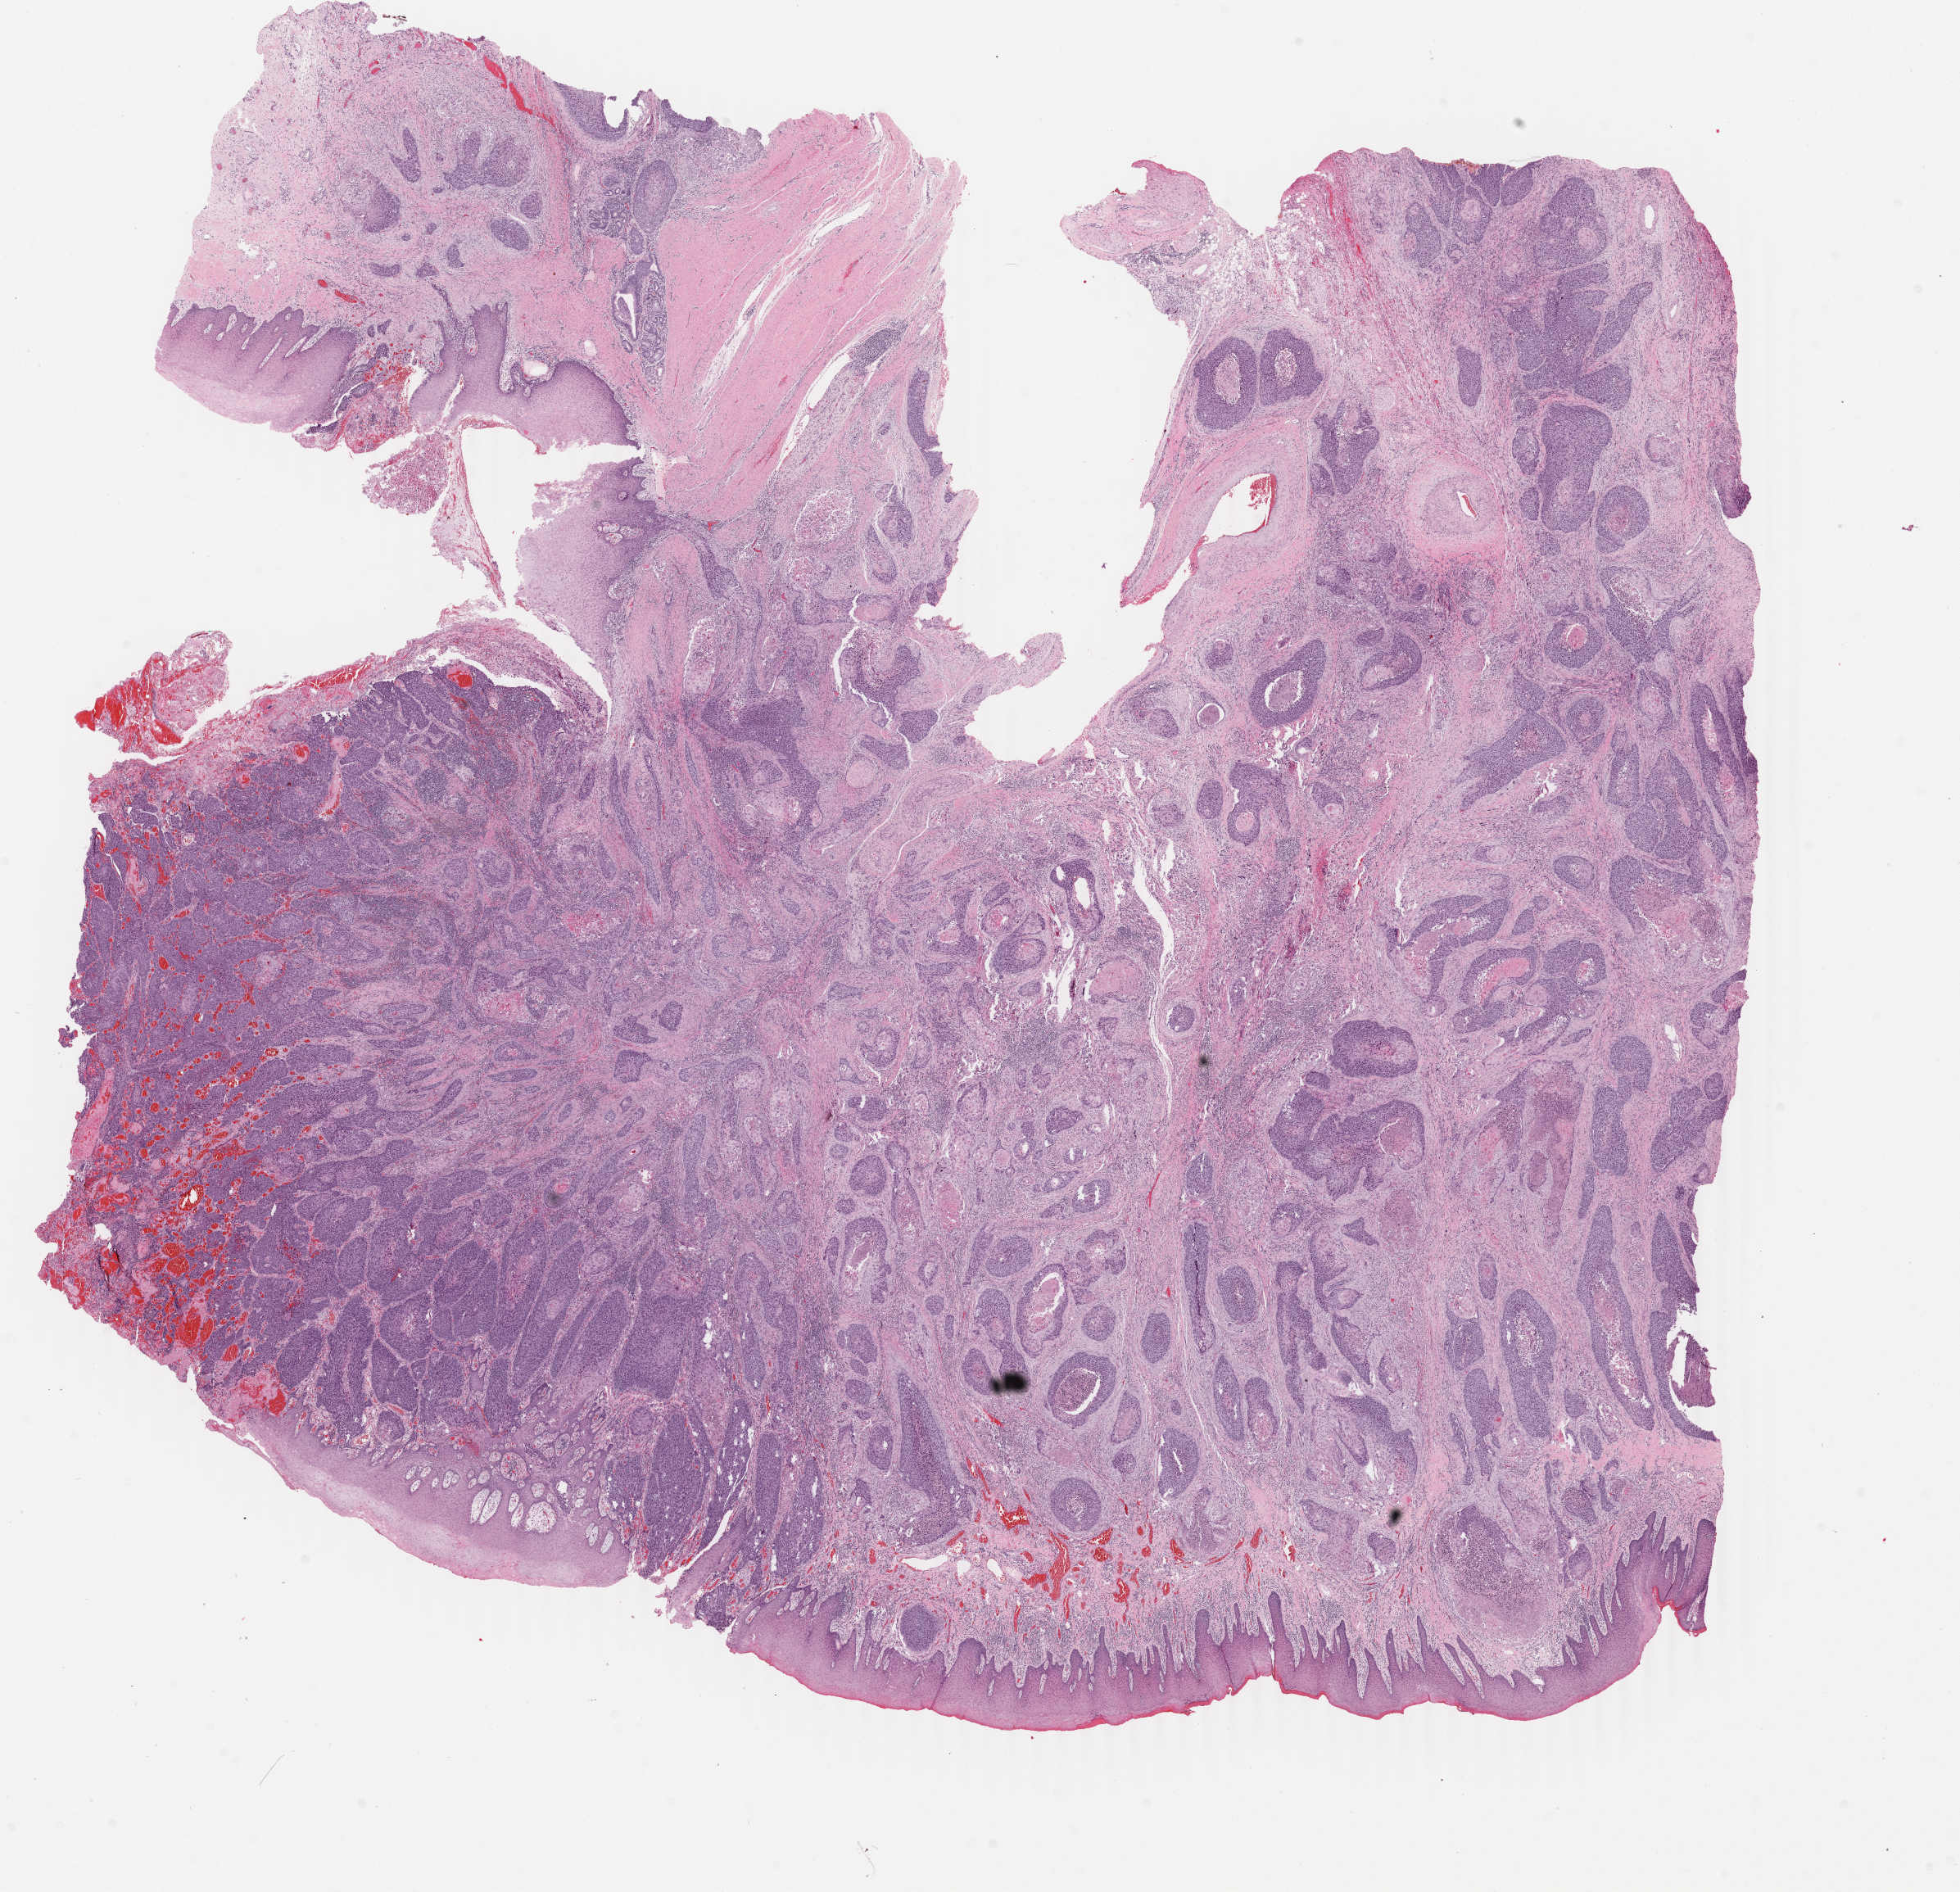
Digitized H&E-stained tissue section (whole slide) — a low-resolution overview of the entire scanned area, about 19.0 x 18.4 mm (slide scanned at 40x). Formalin-fixed paraffin-embedded (FFPE) diagnostic section. Sample: primary tumour, head and neck. Patient: male, age at initial diagnosis 76 years. Histologic grade: G2 (moderately differentiated).
Histologic diagnosis: Squamous cell carcinoma, keratinizing, NOS (tongue, NOS). AJCC pathologic stage: II. TNM: T2 N0 MX.